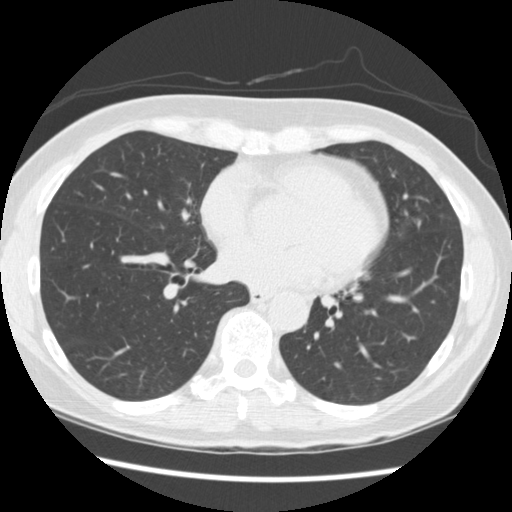
Low-dose screening chest CT, axial slice. Third annual screen. Lung window (W 1500 / L -600 HU). 2.5 mm slice thickness. Standard (soft-tissue) reconstruction kernel (STANDARD). Slice 144 of 262 in the series. Female participant, aged 60 years at enrolment.
Expert-annotated lung lesion, bounding box [x1, y1, x2, y2] px = [394, 204, 438, 243]. Screening reader's record for this exam (one nodule recorded; not confirmed to be the boxed lesion): non-calcified nodule or mass ≥4 mm, lingula, 6 × 5 mm, smooth margins, soft tissue attenuation, pre-existing on the prior screen: yes; interval growth: yes. Participant outcome: lung cancer diagnosed 209 days after this screen — adenocarcinoma, NOS, lingula, poorly differentiated (G3), stage IA (AJCC 6th edition), 6 mm at pathology.